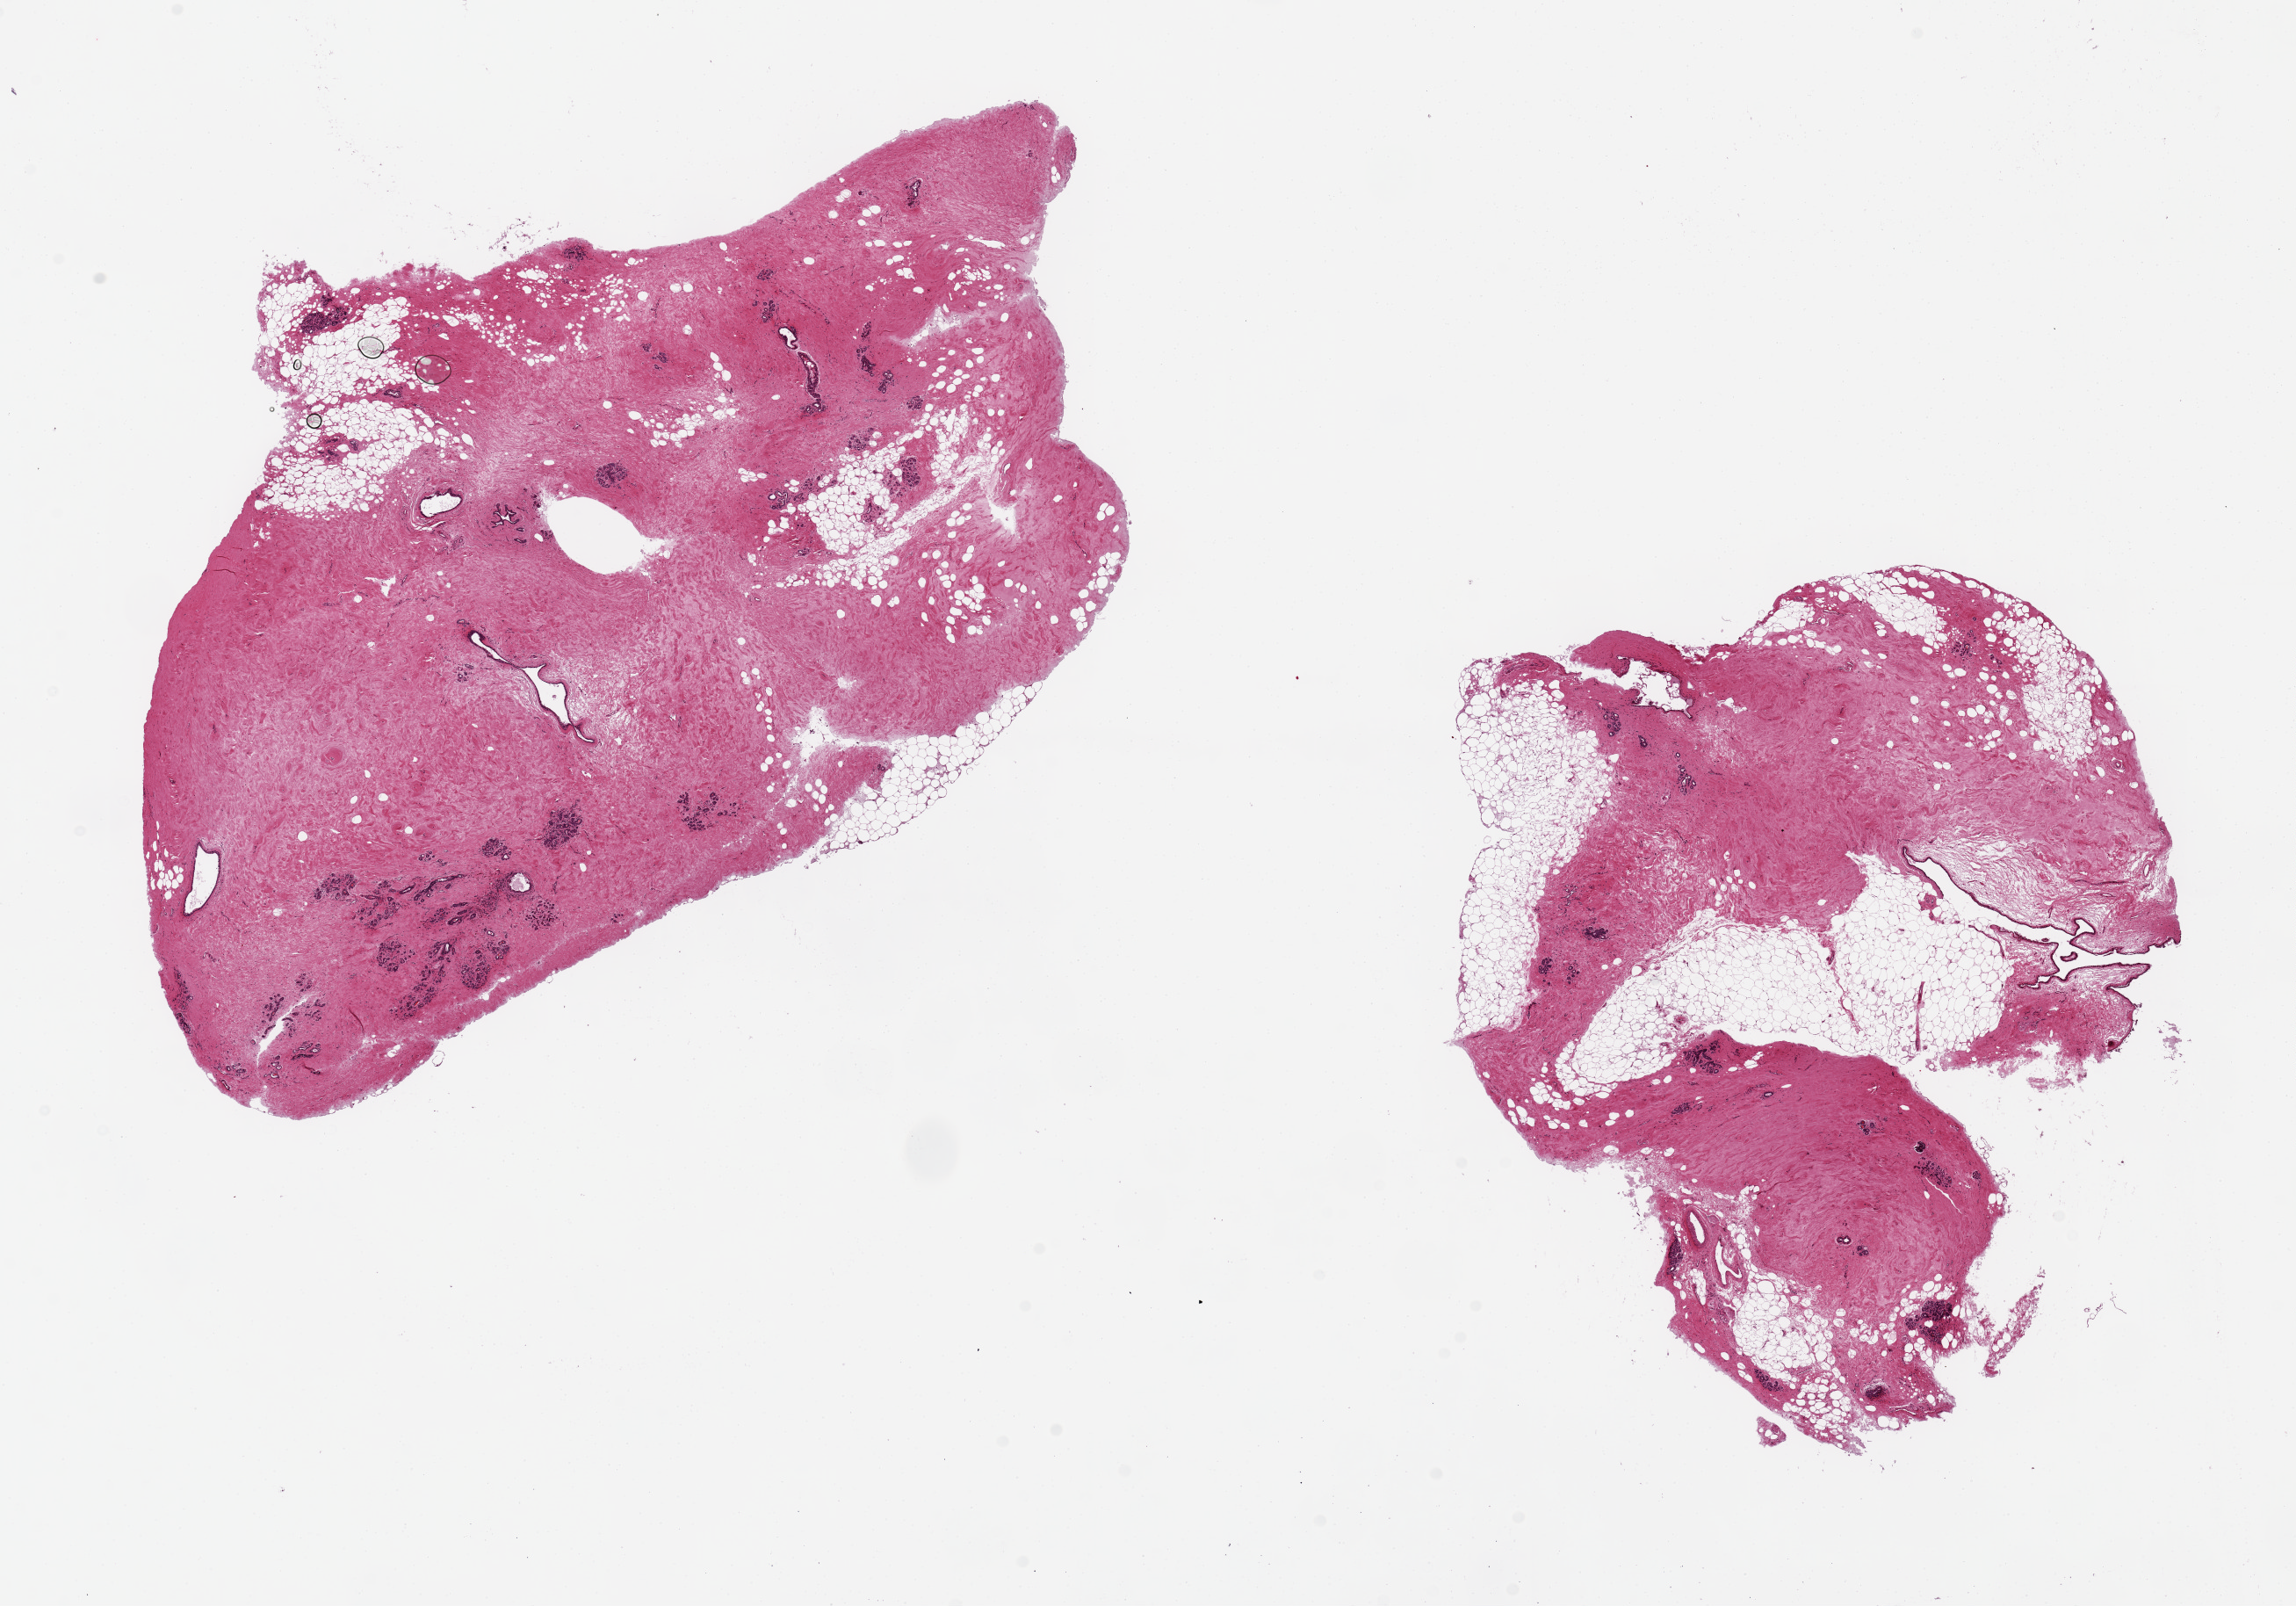
Digitized hematoxylin and eosin (H&E)-stained section, brightfield, shown as a low-resolution overview of the whole scanned area (about 20.7 x 14.5 mm, acquisition: 20x scan); PAXgene-fixed, paraffin-embedded tissue; sampled site (target tissue): breast; donor tissue sample. Donor: female.
Review note (as recorded): 2 pieces. 10x7 & 8x7.5mm; ductal lobular units in fibroadipose tissue.